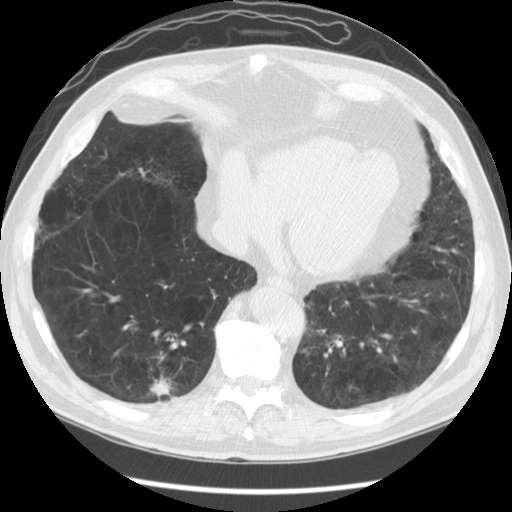
Low-dose screening chest CT, one axial slice. Lung window (W 1500 / L -600 HU). 2.5 mm slice thickness. 512 × 512 image matrix, field of view 370 × 370 mm.
Outlined on this slice (expert manual segmentation):
- lesion 1 (tumor, lower lobe of right lung): box from (x=150, y=376) to (x=172, y=397) px